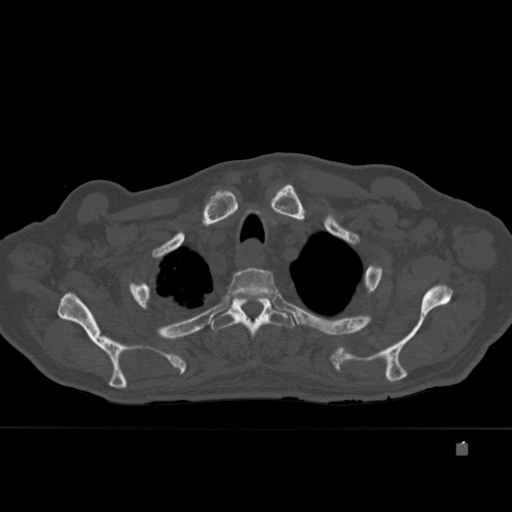
CT including the spine, one axial slice. Position 339 of 451 along the scan axis. Bone window (W 1800 / L 400 HU). 1.5 mm slice thickness. 512 × 512 image matrix, field of view 378 × 378 mm. Male patient, age 75 years. From the clinical record (not read from this slice): primary cancer: prostate.
Outlined on this slice (semi-automatically segmented with operator editing):
- T2 vertebra: bounding box <224,267,281,305> (left, top, right, bottom; pixels)
- T3 vertebra: <210,296,295,339>